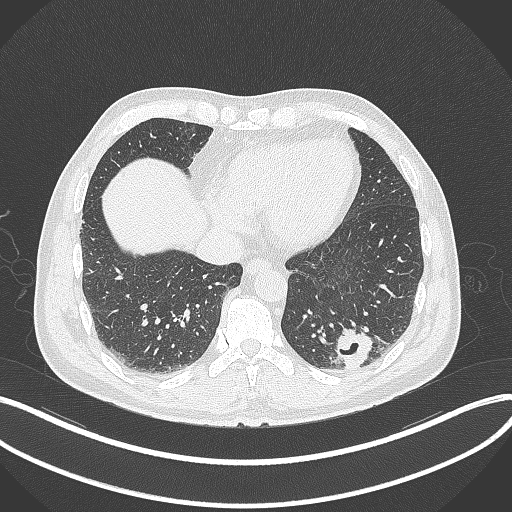
Chest CT, one axial slice; slice 77 of 300 in the series (ordered by position); reconstruction kernel B70f; lung window (W 1500 / L -600 HU); 1 mm slice thickness; 512 × 512 image matrix, field of view 400 × 400 mm. Male patient, age 54 years. From the clinical record (not read from this slice): clinical TNM (as recorded): T1c N0 M1; histopathological grade: G3.
Outlined on this slice (bounding box drawn by a radiologist):
- lung tumour (recorded histology: adenocarcinoma): box from (x=330, y=324) to (x=377, y=371) px